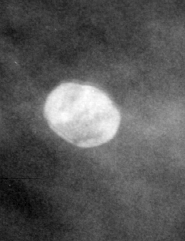
Crop from a digitized film mammogram around one marked abnormality, right breast, CC view.
- Marked abnormality: calcifications, morphology round and regular / eggshell; BI-RADS assessment category 2; benign without callback (not worked up further).